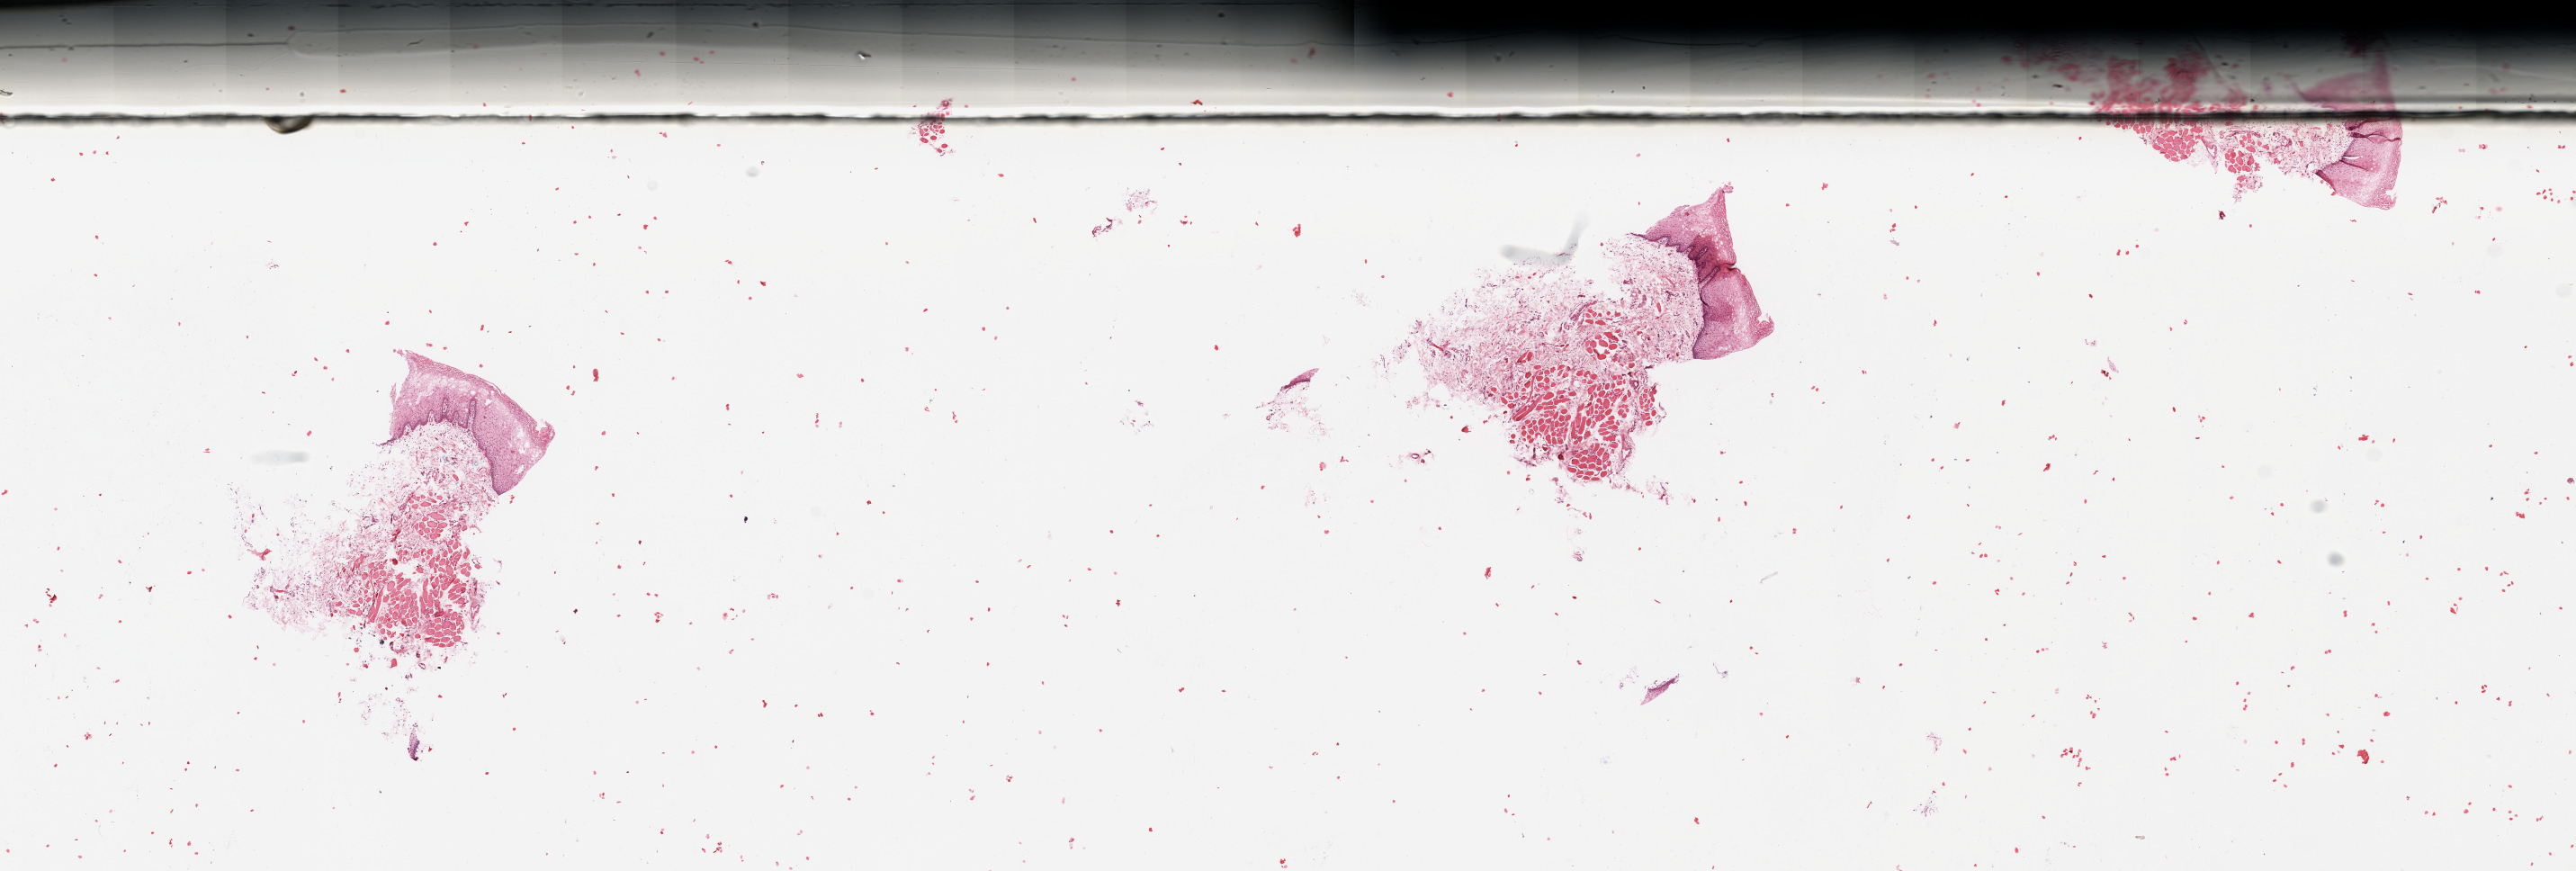
Hematoxylin and eosin (H&E) stained whole-slide image — low-resolution overview of the scanned area, about 22.6 x 7.7 mm, head and neck, normal (non-tumour) tissue. Male, 59 y/o.
This section: normal (non-tumour) tissue from the same patient. Patient diagnosis: Squamous cell carcinoma, NOS (floor of mouth, NOS).